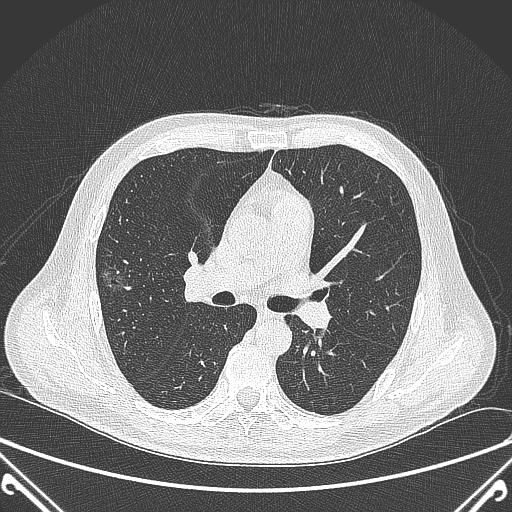
Chest CT, one axial slice; slice 219 of 360 in the series (ordered by position); 120 kVp; lung window (W 1500 / L -600 HU); 1 mm slice thickness; 512 × 512 image matrix, field of view 380 × 380 mm. Male patient, age 64 years. From the clinical record (not read from this slice): clinical TNM (as recorded): T1c N0 M0; histopathological grade: G2.
Structures marked on this image (bounding box drawn by a radiologist):
- lung tumour (recorded histology: adenocarcinoma): bounding box [x1, y1, x2, y2] px = [95, 259, 135, 297]